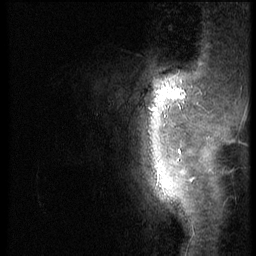
Breast MRI (dynamic contrast-enhanced), one sagittal slice; slice 8 of 56 in the series (ordered by position); 3 images stored at this slice position (order not interpretable as contrast timing); 1.5 T; TE 4.2 ms, TR 9 ms; 2.5 mm slice thickness; 256 × 256 image matrix. Patient: female, 46 years. Case-level facts recorded for this patient, not image findings: setting: breast cancer imaged before/during neoadjuvant chemotherapy; receptor status: HER2-positive.
Annotated regions visible in this slice (semi-automatic segmentation, software-assisted and operator-edited):
- analysis volume of interest (the breast-tissue region the enhancement analysis was run in; not a lesion): bounding box <99,68,190,143> (left, top, right, bottom; pixels)
- tumour enhancement mask (voxels above the 140 % enhancement threshold inside the analysis volume of interest): <174,95,185,99>